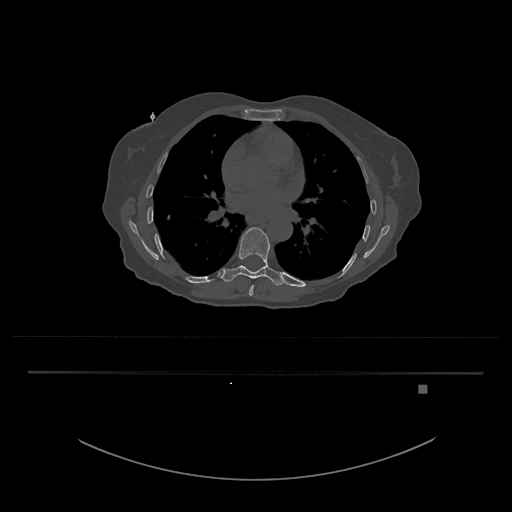
CT including the spine, one axial slice; slice 765 of 797 in the series (ordered by position); reconstruction kernel Br40s/3; bone window (W 1800 / L 400 HU); 0.5 mm slice thickness; 512 × 512 image matrix, field of view 500 × 500 mm. Patient: female, 57 years. Case-level facts recorded for this patient, not image findings: primary cancer: cervical.
Annotated regions visible in this slice (semi-automatic segmentation, software-assisted and operator-edited):
- T8 vertebra: box from (x=249, y=284) to (x=254, y=296) px
- T9 vertebra: (x=221, y=227)–(x=286, y=286)